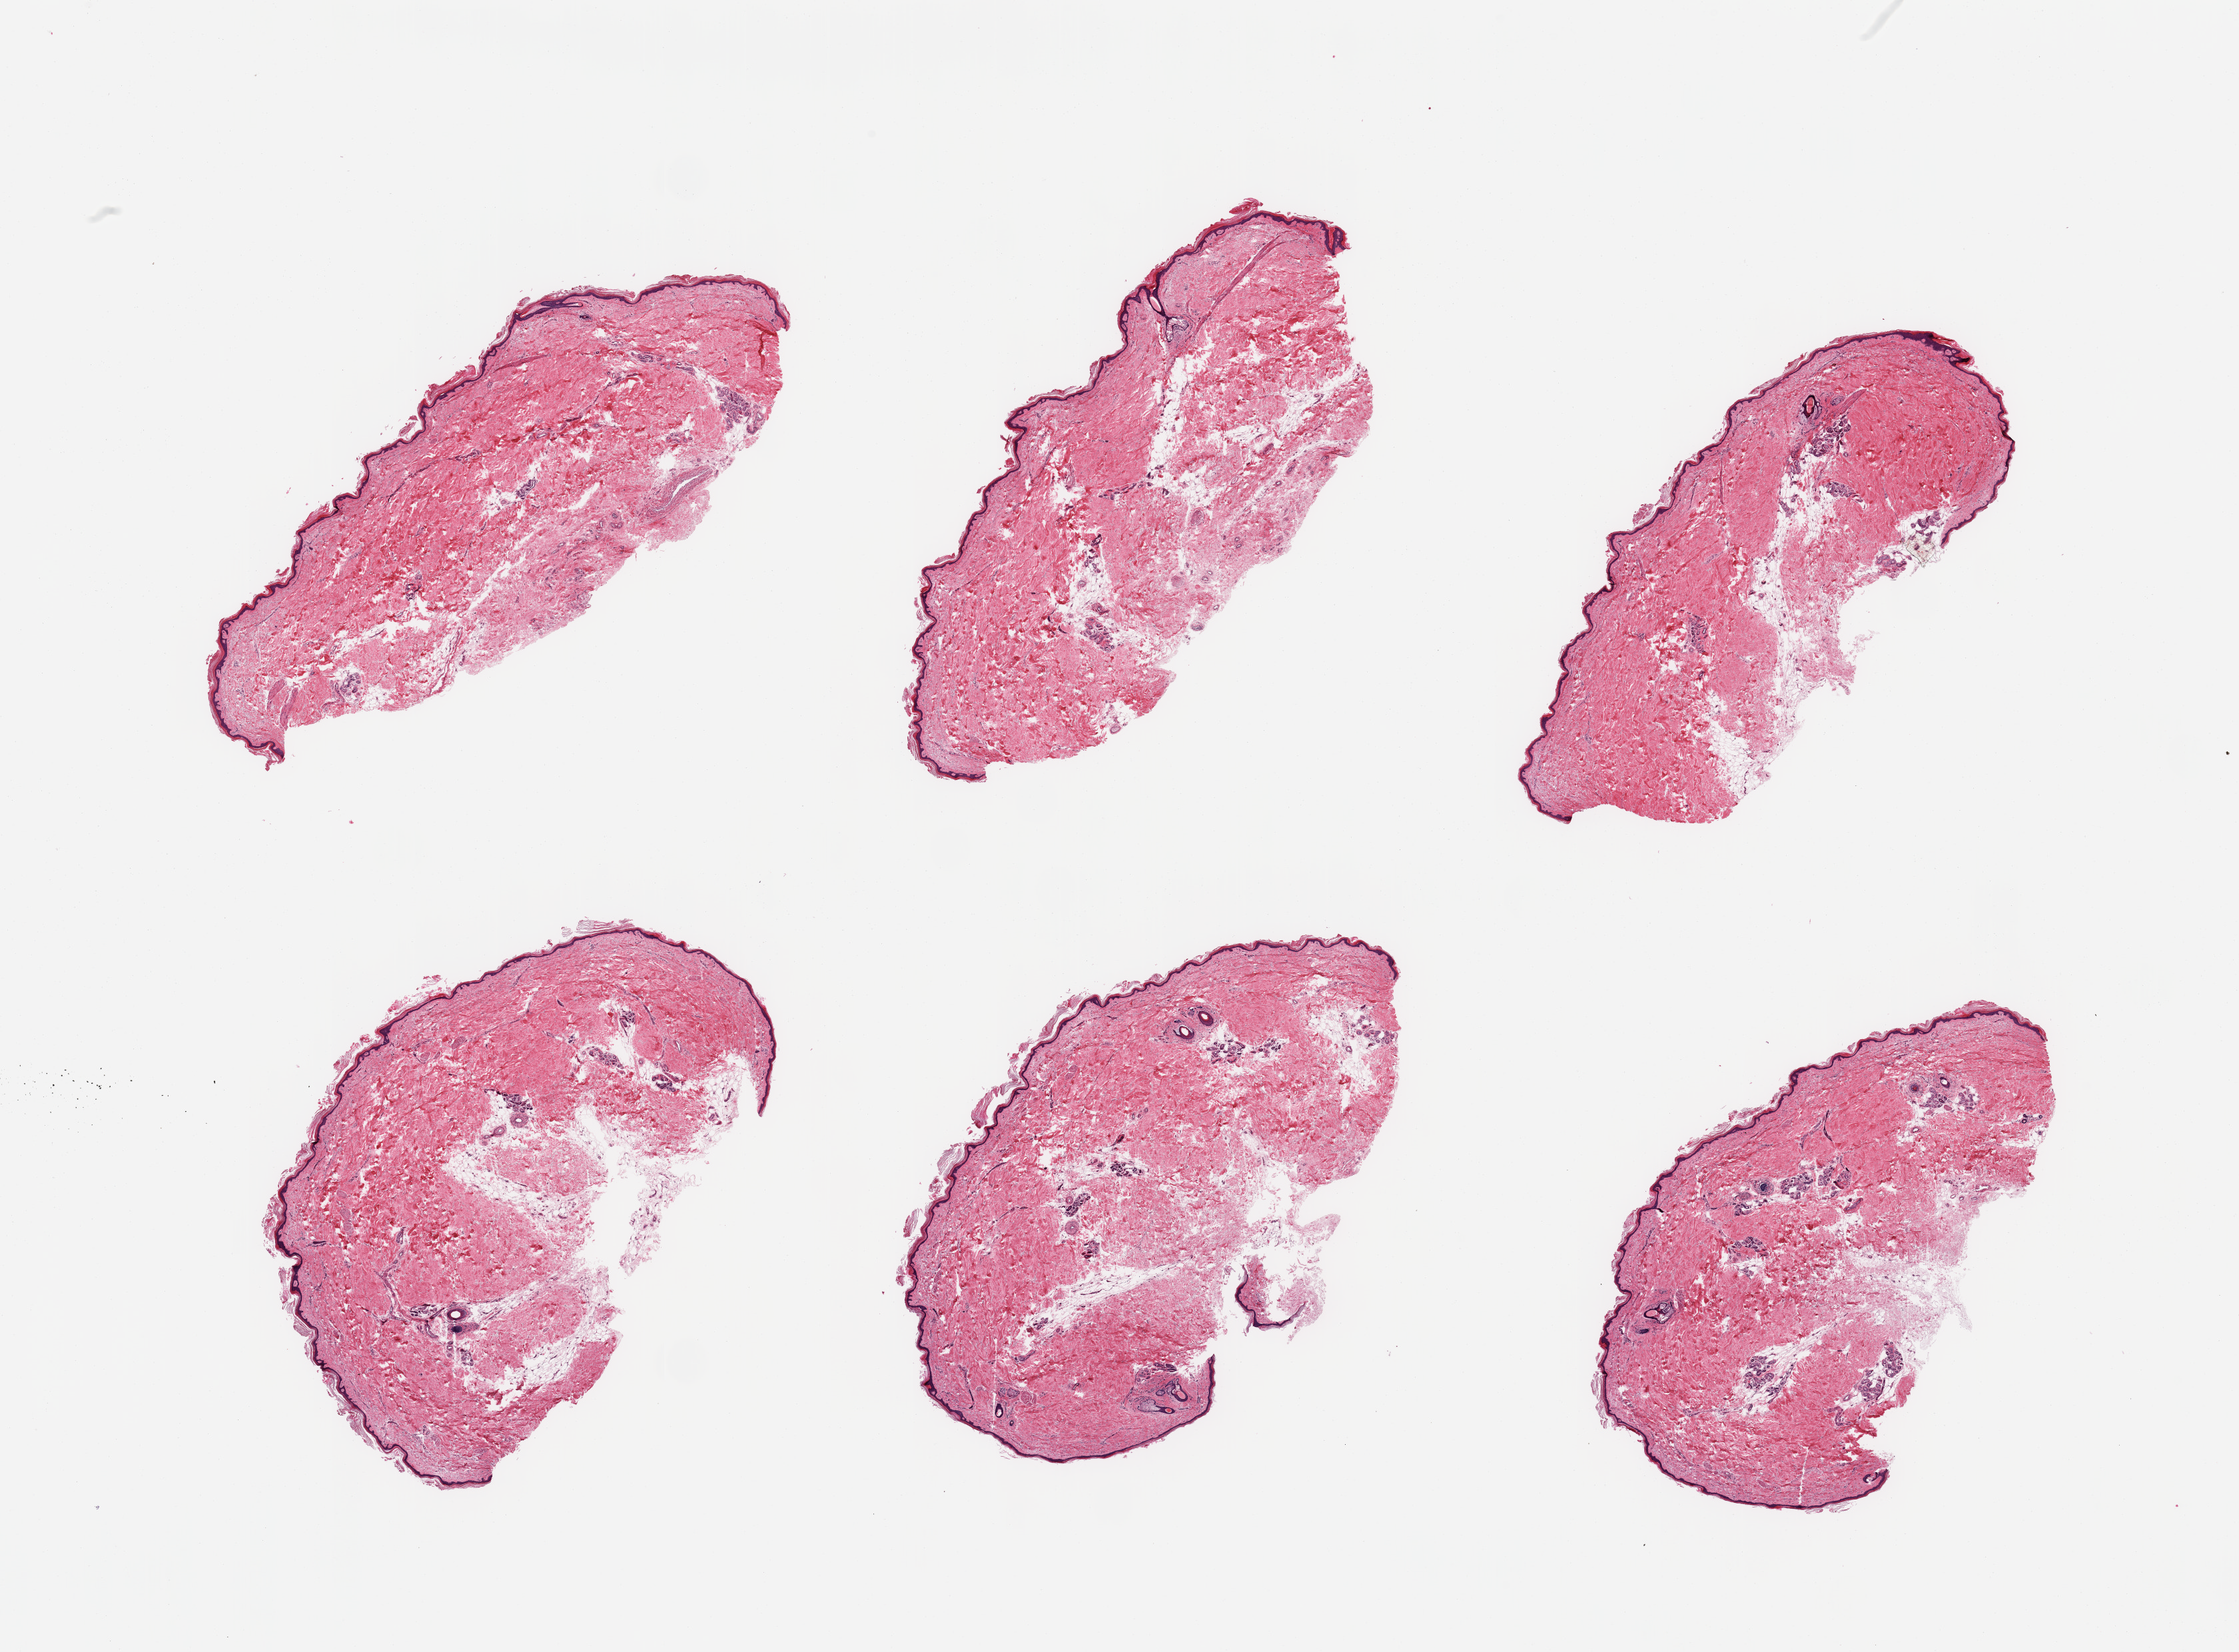
Whole-slide image, hematoxylin and eosin (H&E) stain — shown as a low-resolution overview of the whole scanned area (about 26.6 x 19.6 mm). Donor sex: male.
Specimen: PAXgene-fixed, paraffin-embedded tissue; target tissue: skin of lower leg; donor tissue sample.